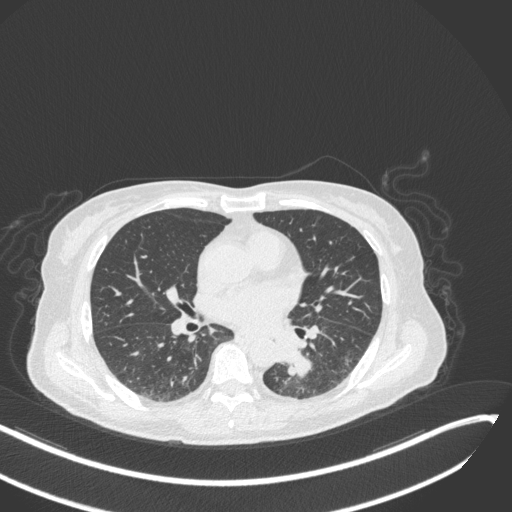
Chest CT, one axial slice. Slice 132 of 342 in the series (ordered by position). 120 kVp. Lung window (W 1500 / L -600 HU). 1 mm slice thickness. 512 × 512 image matrix. Patient: female, 64 years. From the clinical record (not read from this slice): clinical TNM (as recorded): T3 N1 M1; histopathological grade: G3.
Outlined on this slice (rectangle marked by the reading radiologist):
- lung tumour (recorded histology: small cell carcinoma): bounding box (x1, y1, x2, y2) in pixels: (279, 346, 315, 385)